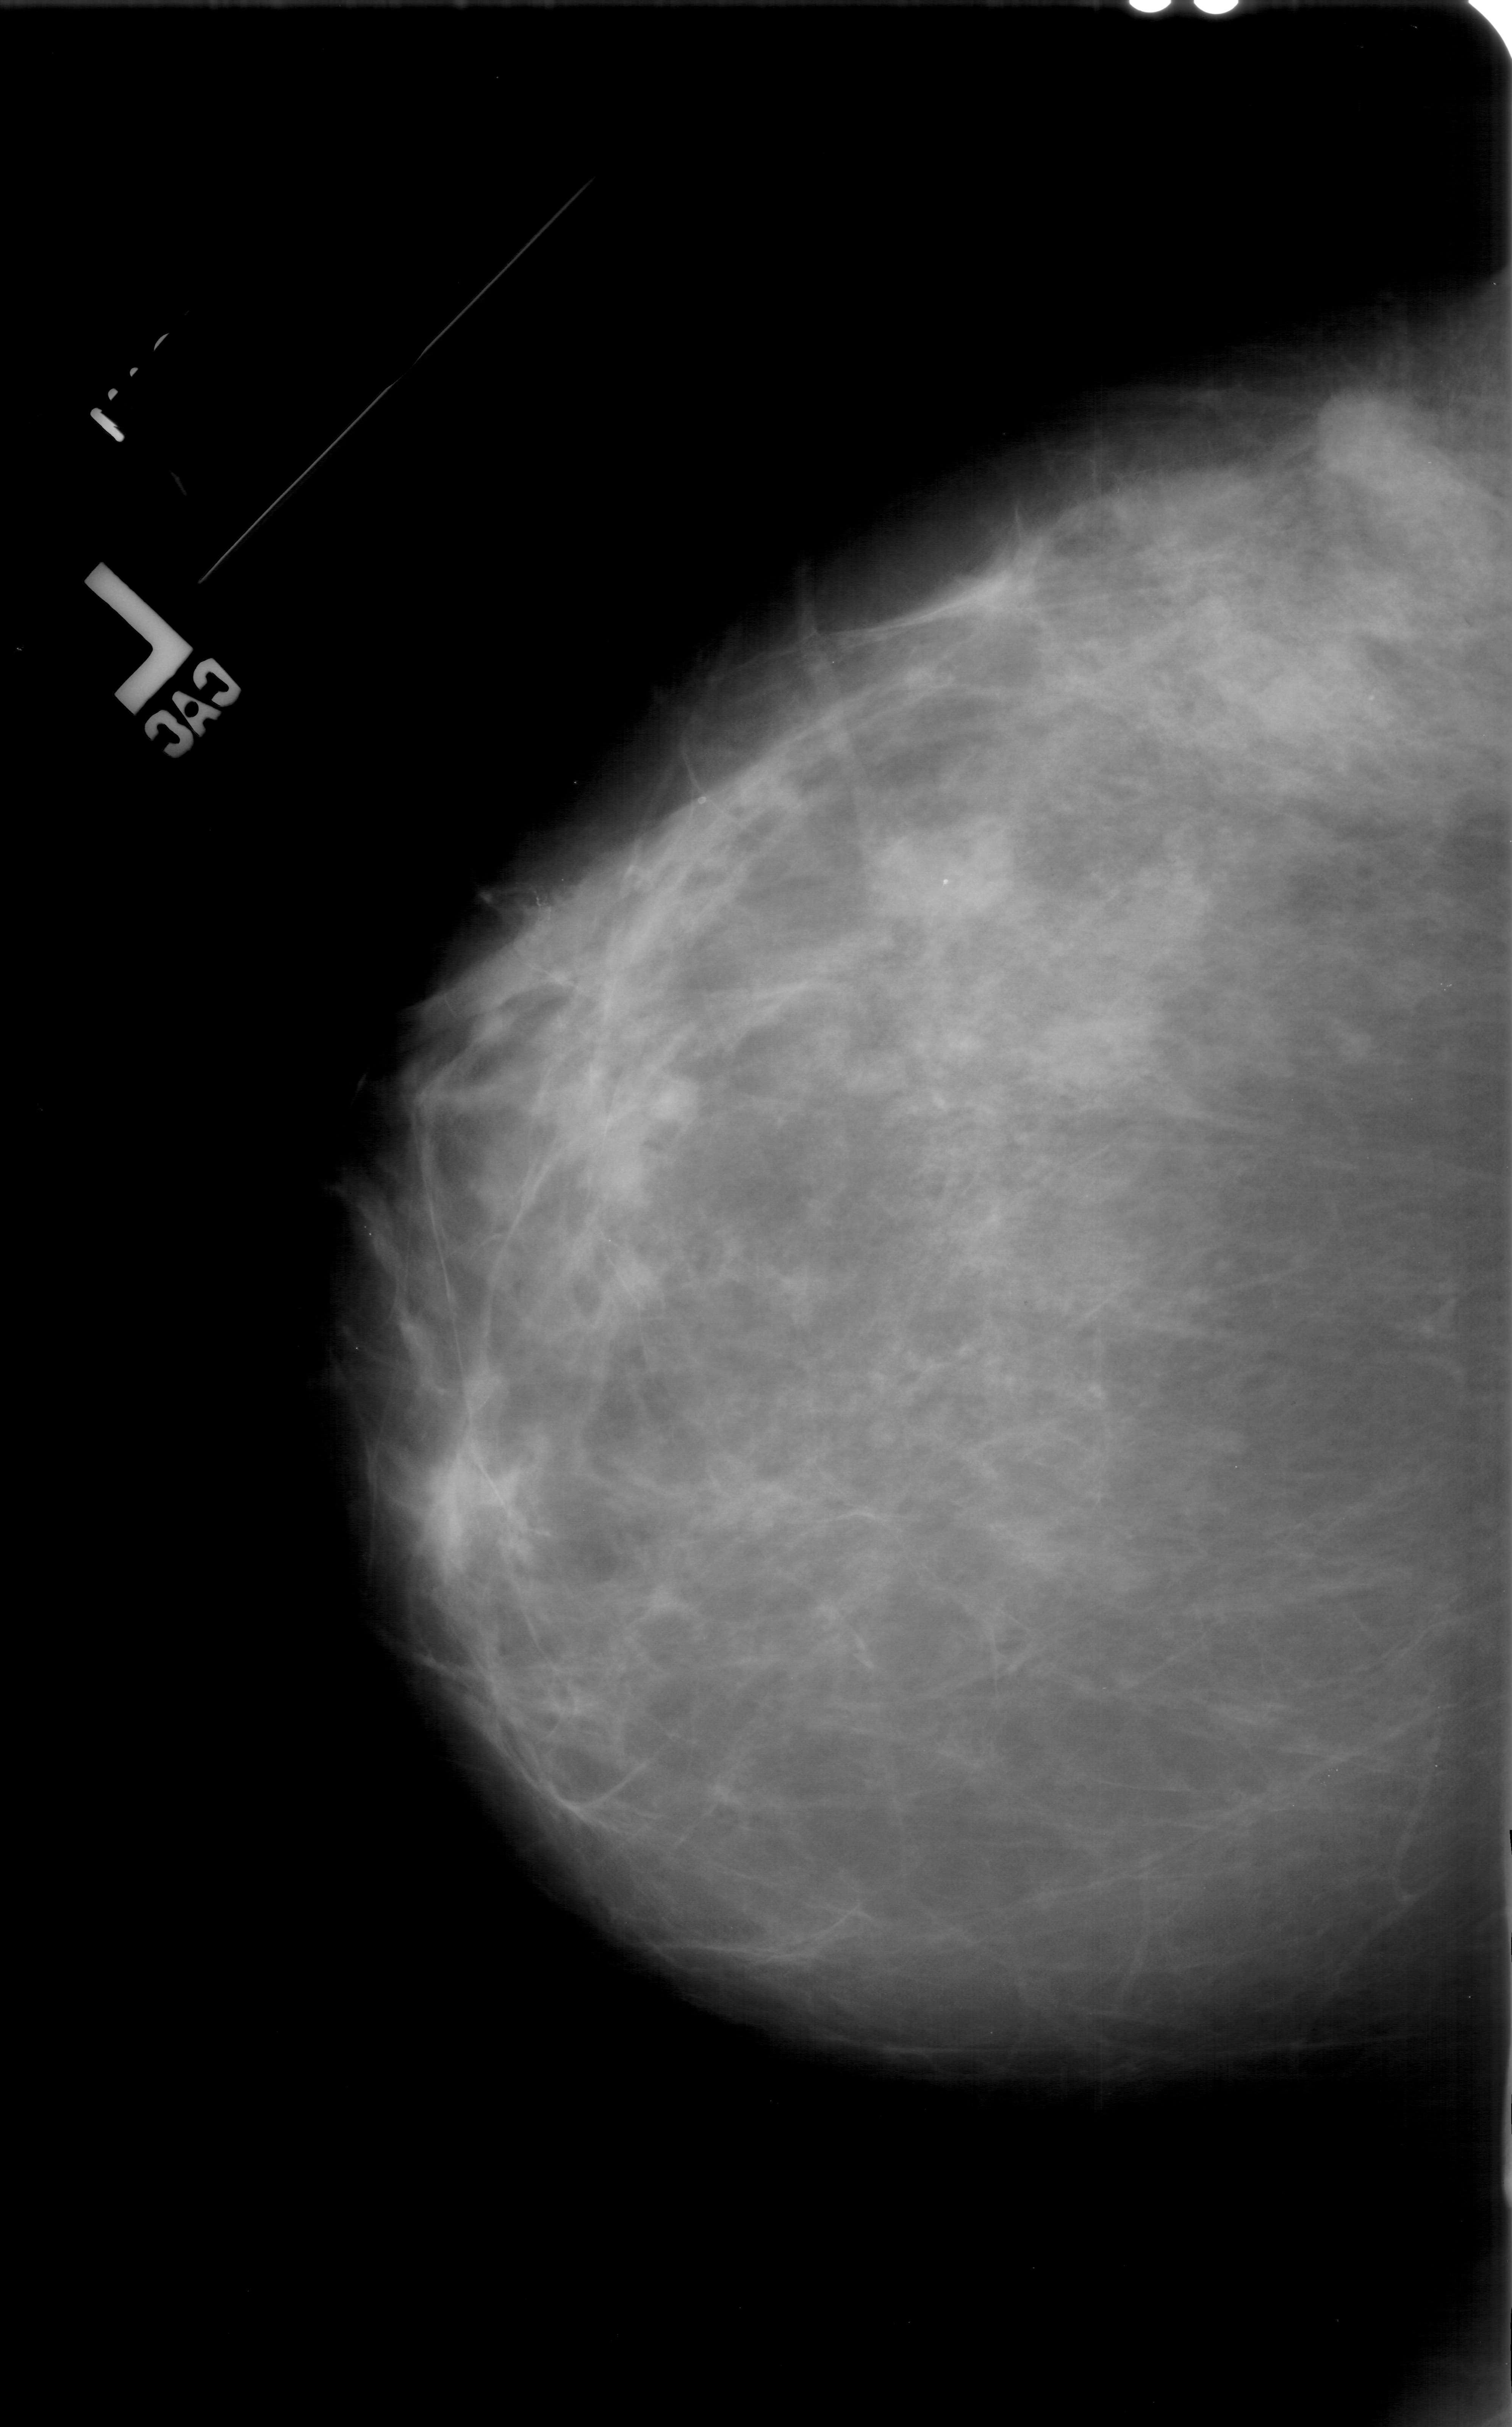
Mammogram (digitized film), left breast, CC view, BI-RADS breast density category 3 (scale 1–4).
Marked abnormality: mass, shape lobulated, margins ill defined; BI-RADS assessment category 4; pathology (as recorded): malignant.